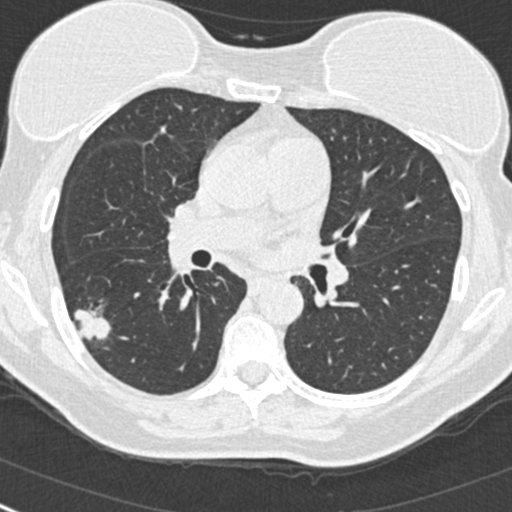
Low-dose screening chest CT, one axial slice. Position 147 of 268 along the scan axis. 120 kVp. Lung window (W 1500 / L -600 HU). 512 × 512 image matrix.
Structures marked on this image (expert manual segmentation):
- lesion 1 (tumor, upper lobe of right lung): bounding box <74,308,111,340> (left, top, right, bottom; pixels)